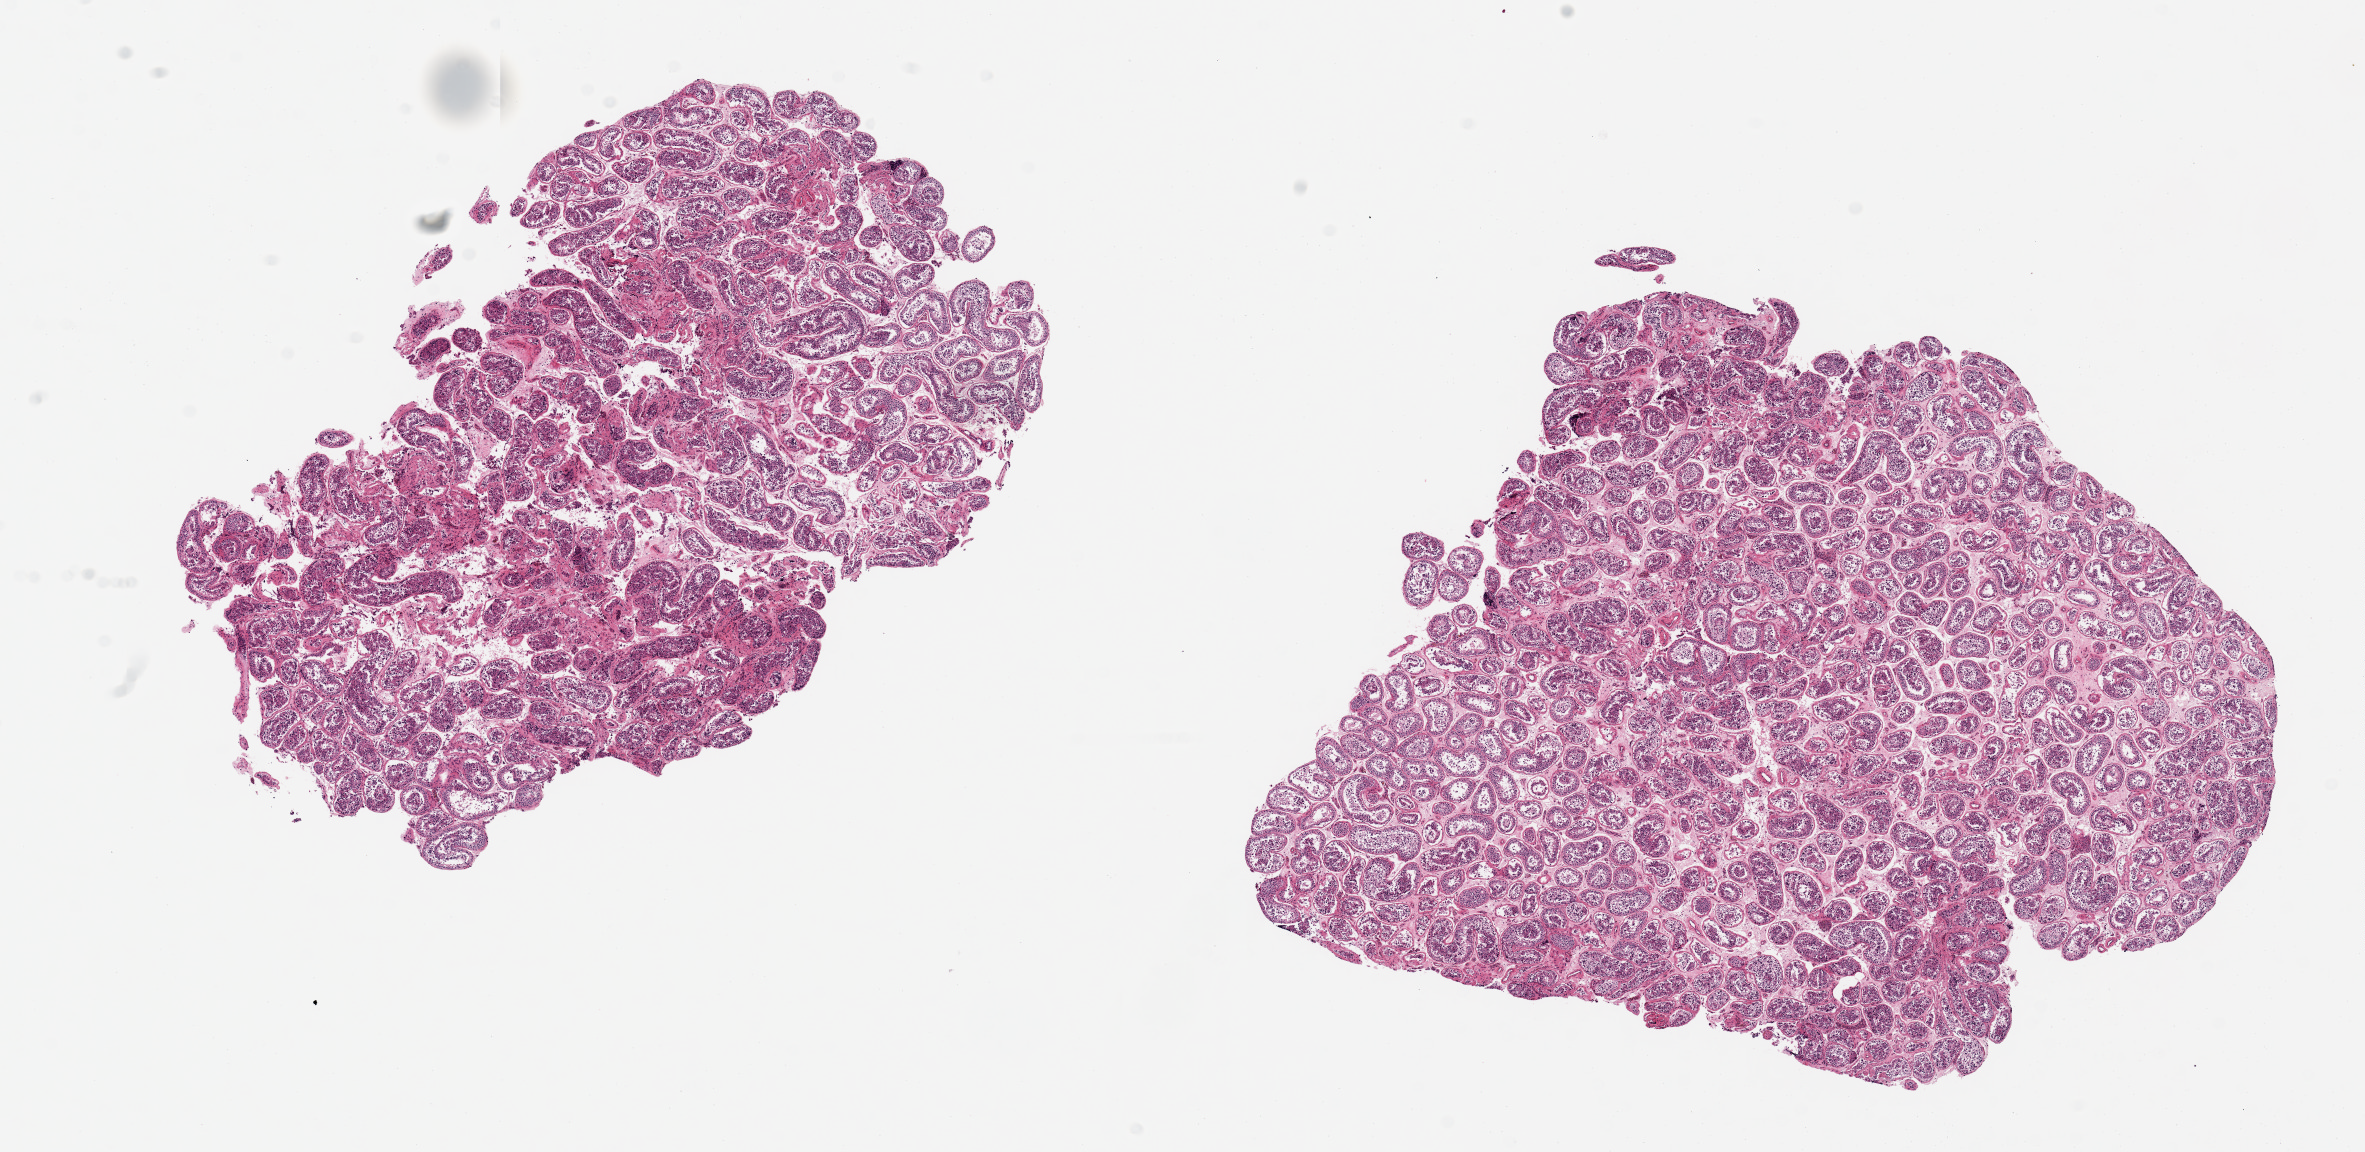
Digitized H&E-stained section, brightfield — a low-resolution overview of the entire scanned area, about 18.7 x 9.1 mm (slide scanned at 20x), PAXgene-fixed, paraffin-embedded tissue, section of testis (target tissue), tissue donor sample.
• review note (as recorded): 2 pieces, 7x5 & 7x6mm; slightly decreased spermatogensis